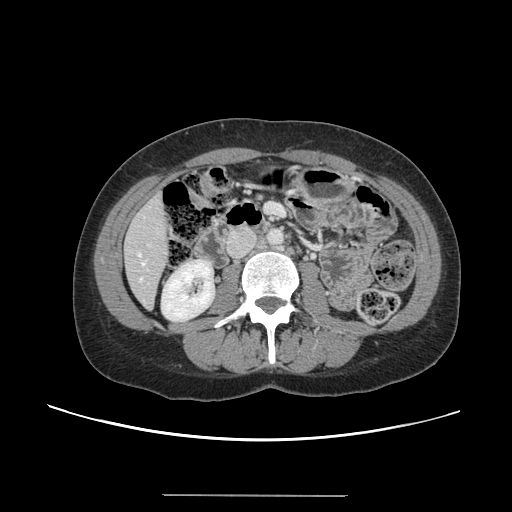
Contrast-enhanced abdominal CT, one axial slice. 120 kVp. Soft-tissue window (W 400 / L 40 HU). 2.5 mm slice thickness. 512 × 512 image matrix, field of view 380 × 380 mm. Female patient, age 53 years. Case-level facts recorded for this patient, not image findings: diagnosis: colorectal cancer liver metastases, imaged before liver resection; multiple liver metastases: yes; largest metastasis: 1.1 cm; disease in both lobes: no.
Structures marked on this image (manually delineated by an expert):
- hepatic veins: box from (x=138, y=254) to (x=145, y=280) px
- liver: (x=124, y=194)–(x=169, y=308)
- planned liver remnant (the part of the liver to remain after resection): (x=125, y=193)–(x=169, y=307)
- portal vein (with intrahepatic branches): (x=148, y=244)–(x=151, y=247)